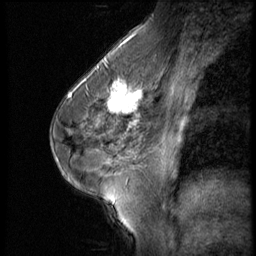
Breast MRI (dynamic contrast-enhanced), one sagittal slice; position 33 of 56 along the scan axis; 3 images stored at this slice position (order not interpretable as contrast timing); 1.5 T; TE 4.2 ms, TR 9 ms; 2.5 mm slice thickness; 256 × 256 image matrix, field of view 180 × 180 mm. Patient: female, 45 years. Case-level facts recorded for this patient, not image findings: setting: breast cancer imaged before/during neoadjuvant chemotherapy; receptor status: HR-positive, HER2-negative.
Annotated regions visible in this slice (semi-automatic segmentation, software-assisted and operator-edited):
- analysis volume of interest (the breast-tissue region the enhancement analysis was run in; not a lesion): bounding box <102,77,166,129> (left, top, right, bottom; pixels)
- tumour enhancement mask (voxels above the 140 % enhancement threshold inside the analysis volume of interest): <106,79,150,129>